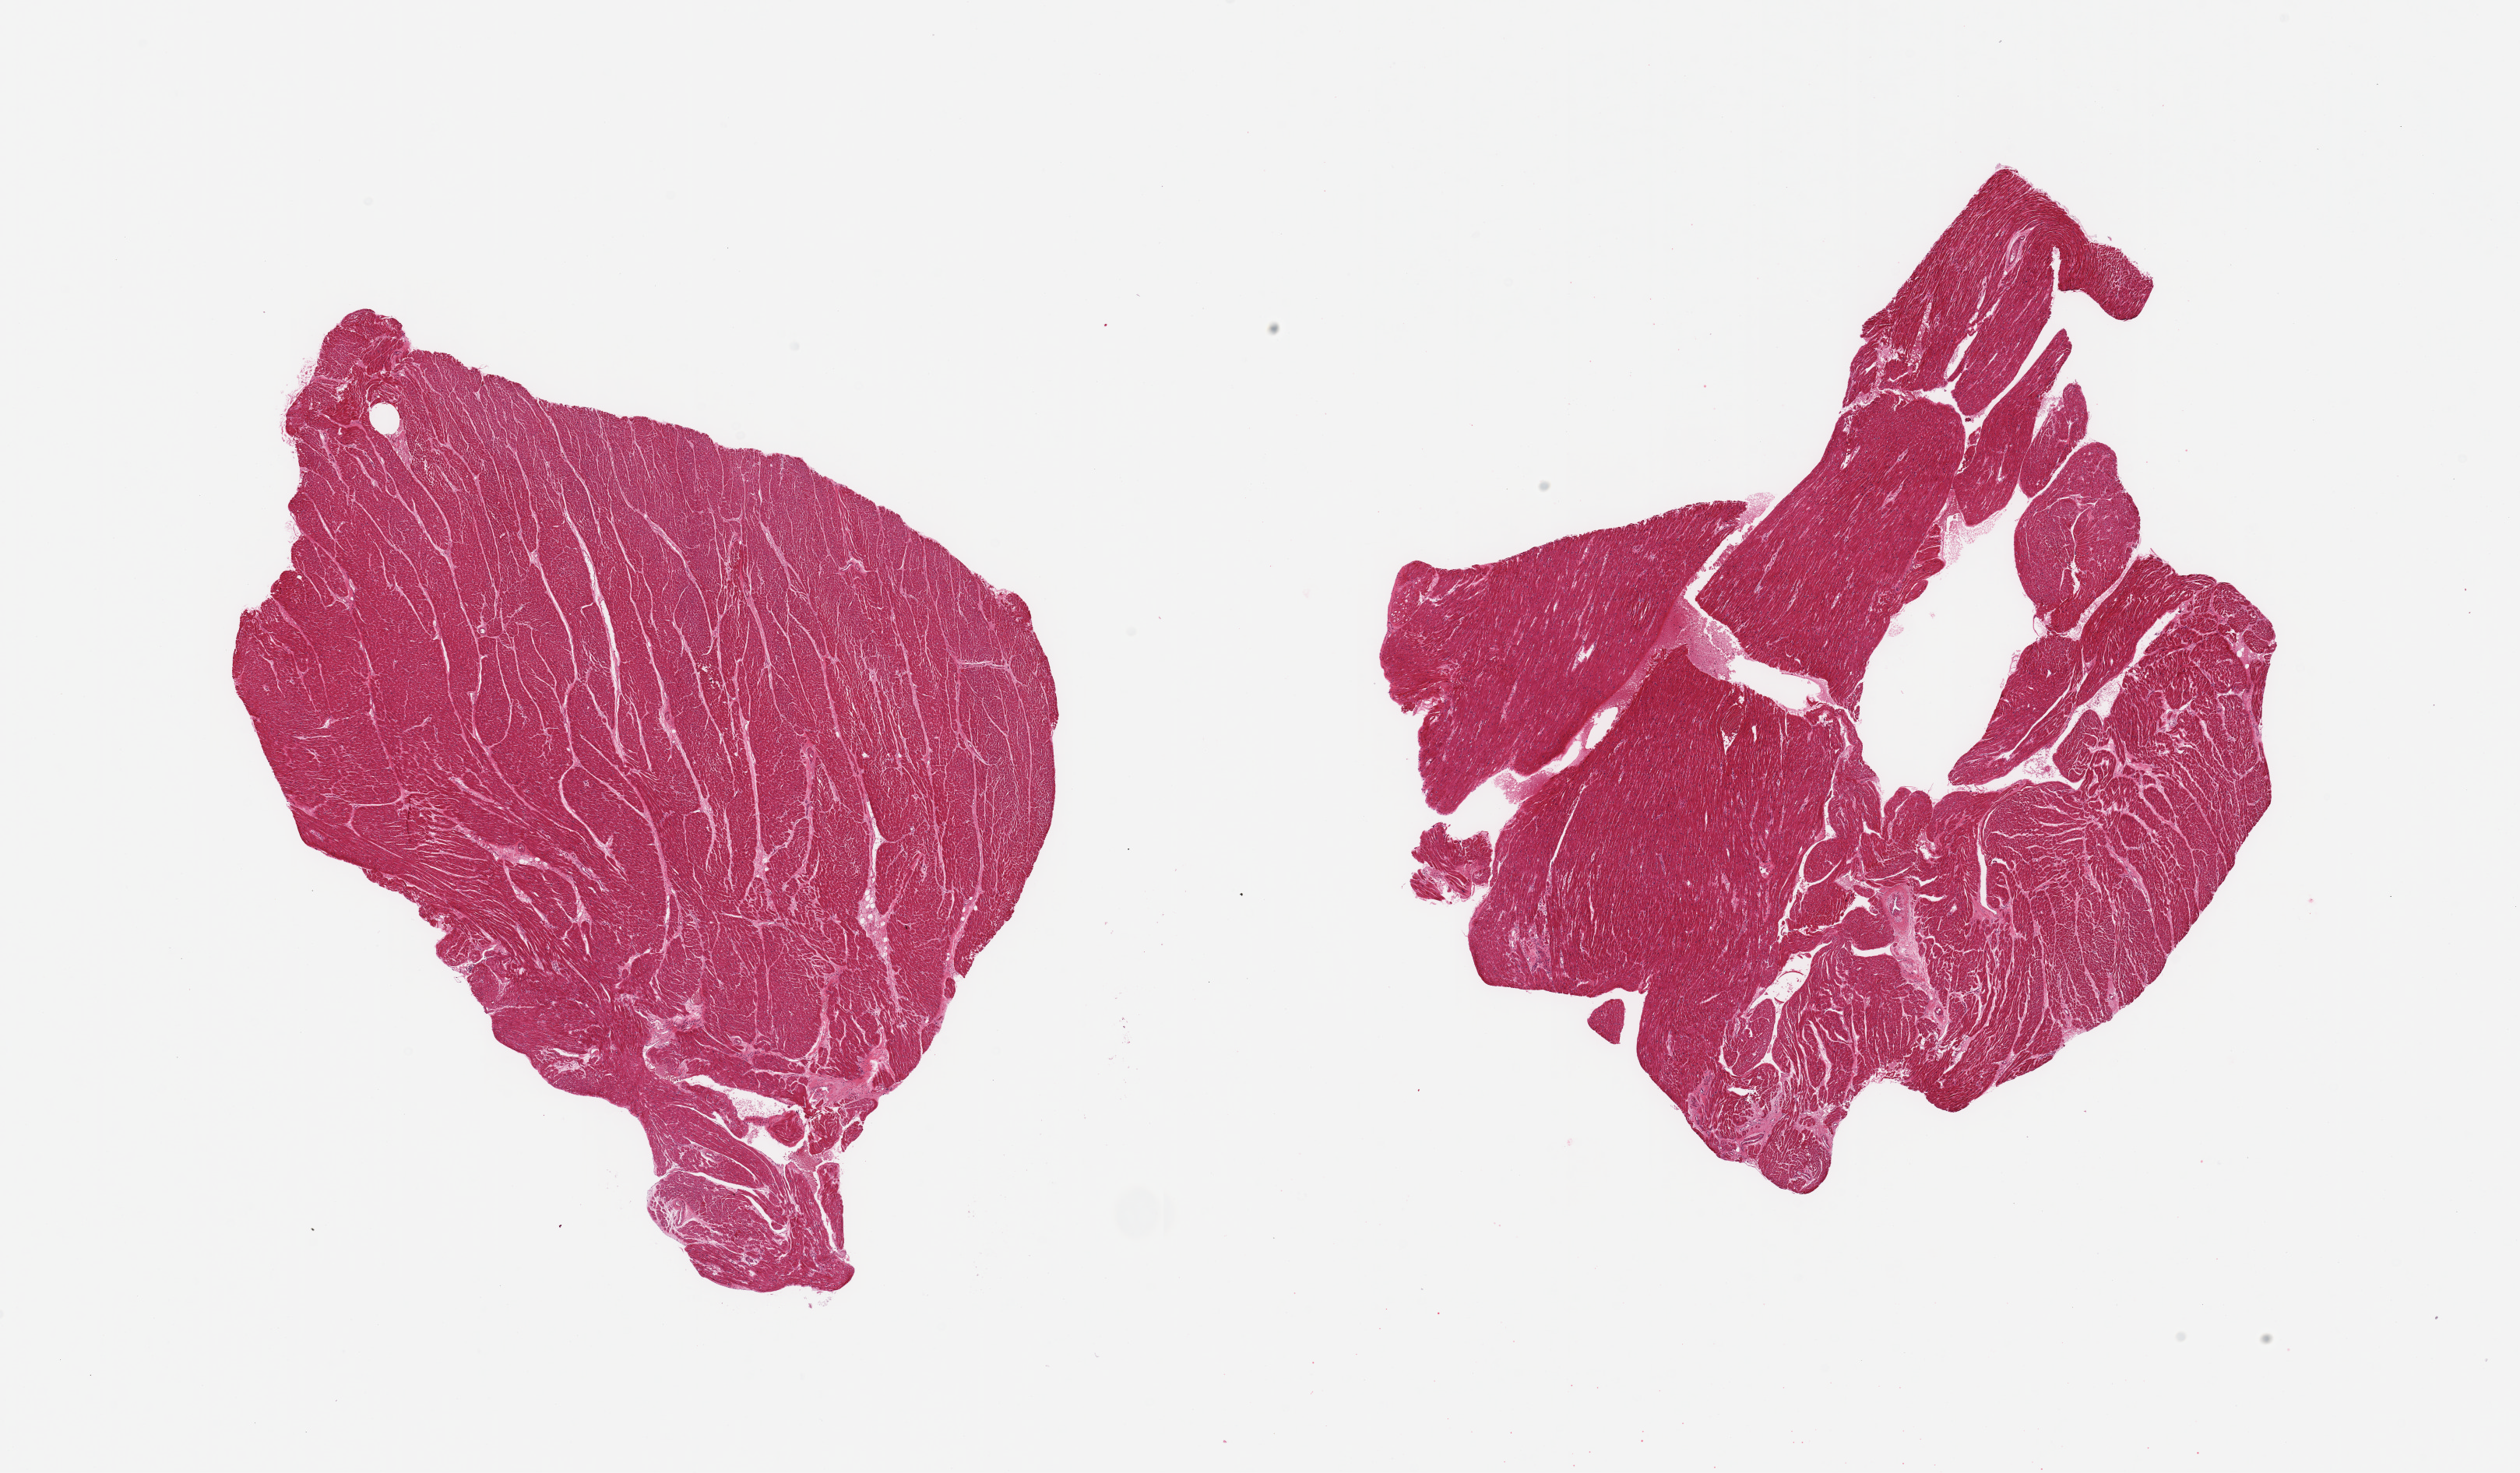
Digitized haematoxylin and eosin-stained section, a low-resolution overview of the entire scanned area, about 25.6 x 15.0 mm (acquisition: 20x scan). PAXgene-fixed, paraffin-embedded tissue. Target tissue: heart. Donor tissue sample. Donor: male.
Reviewer comment on this tissue sample: 2 pieces.